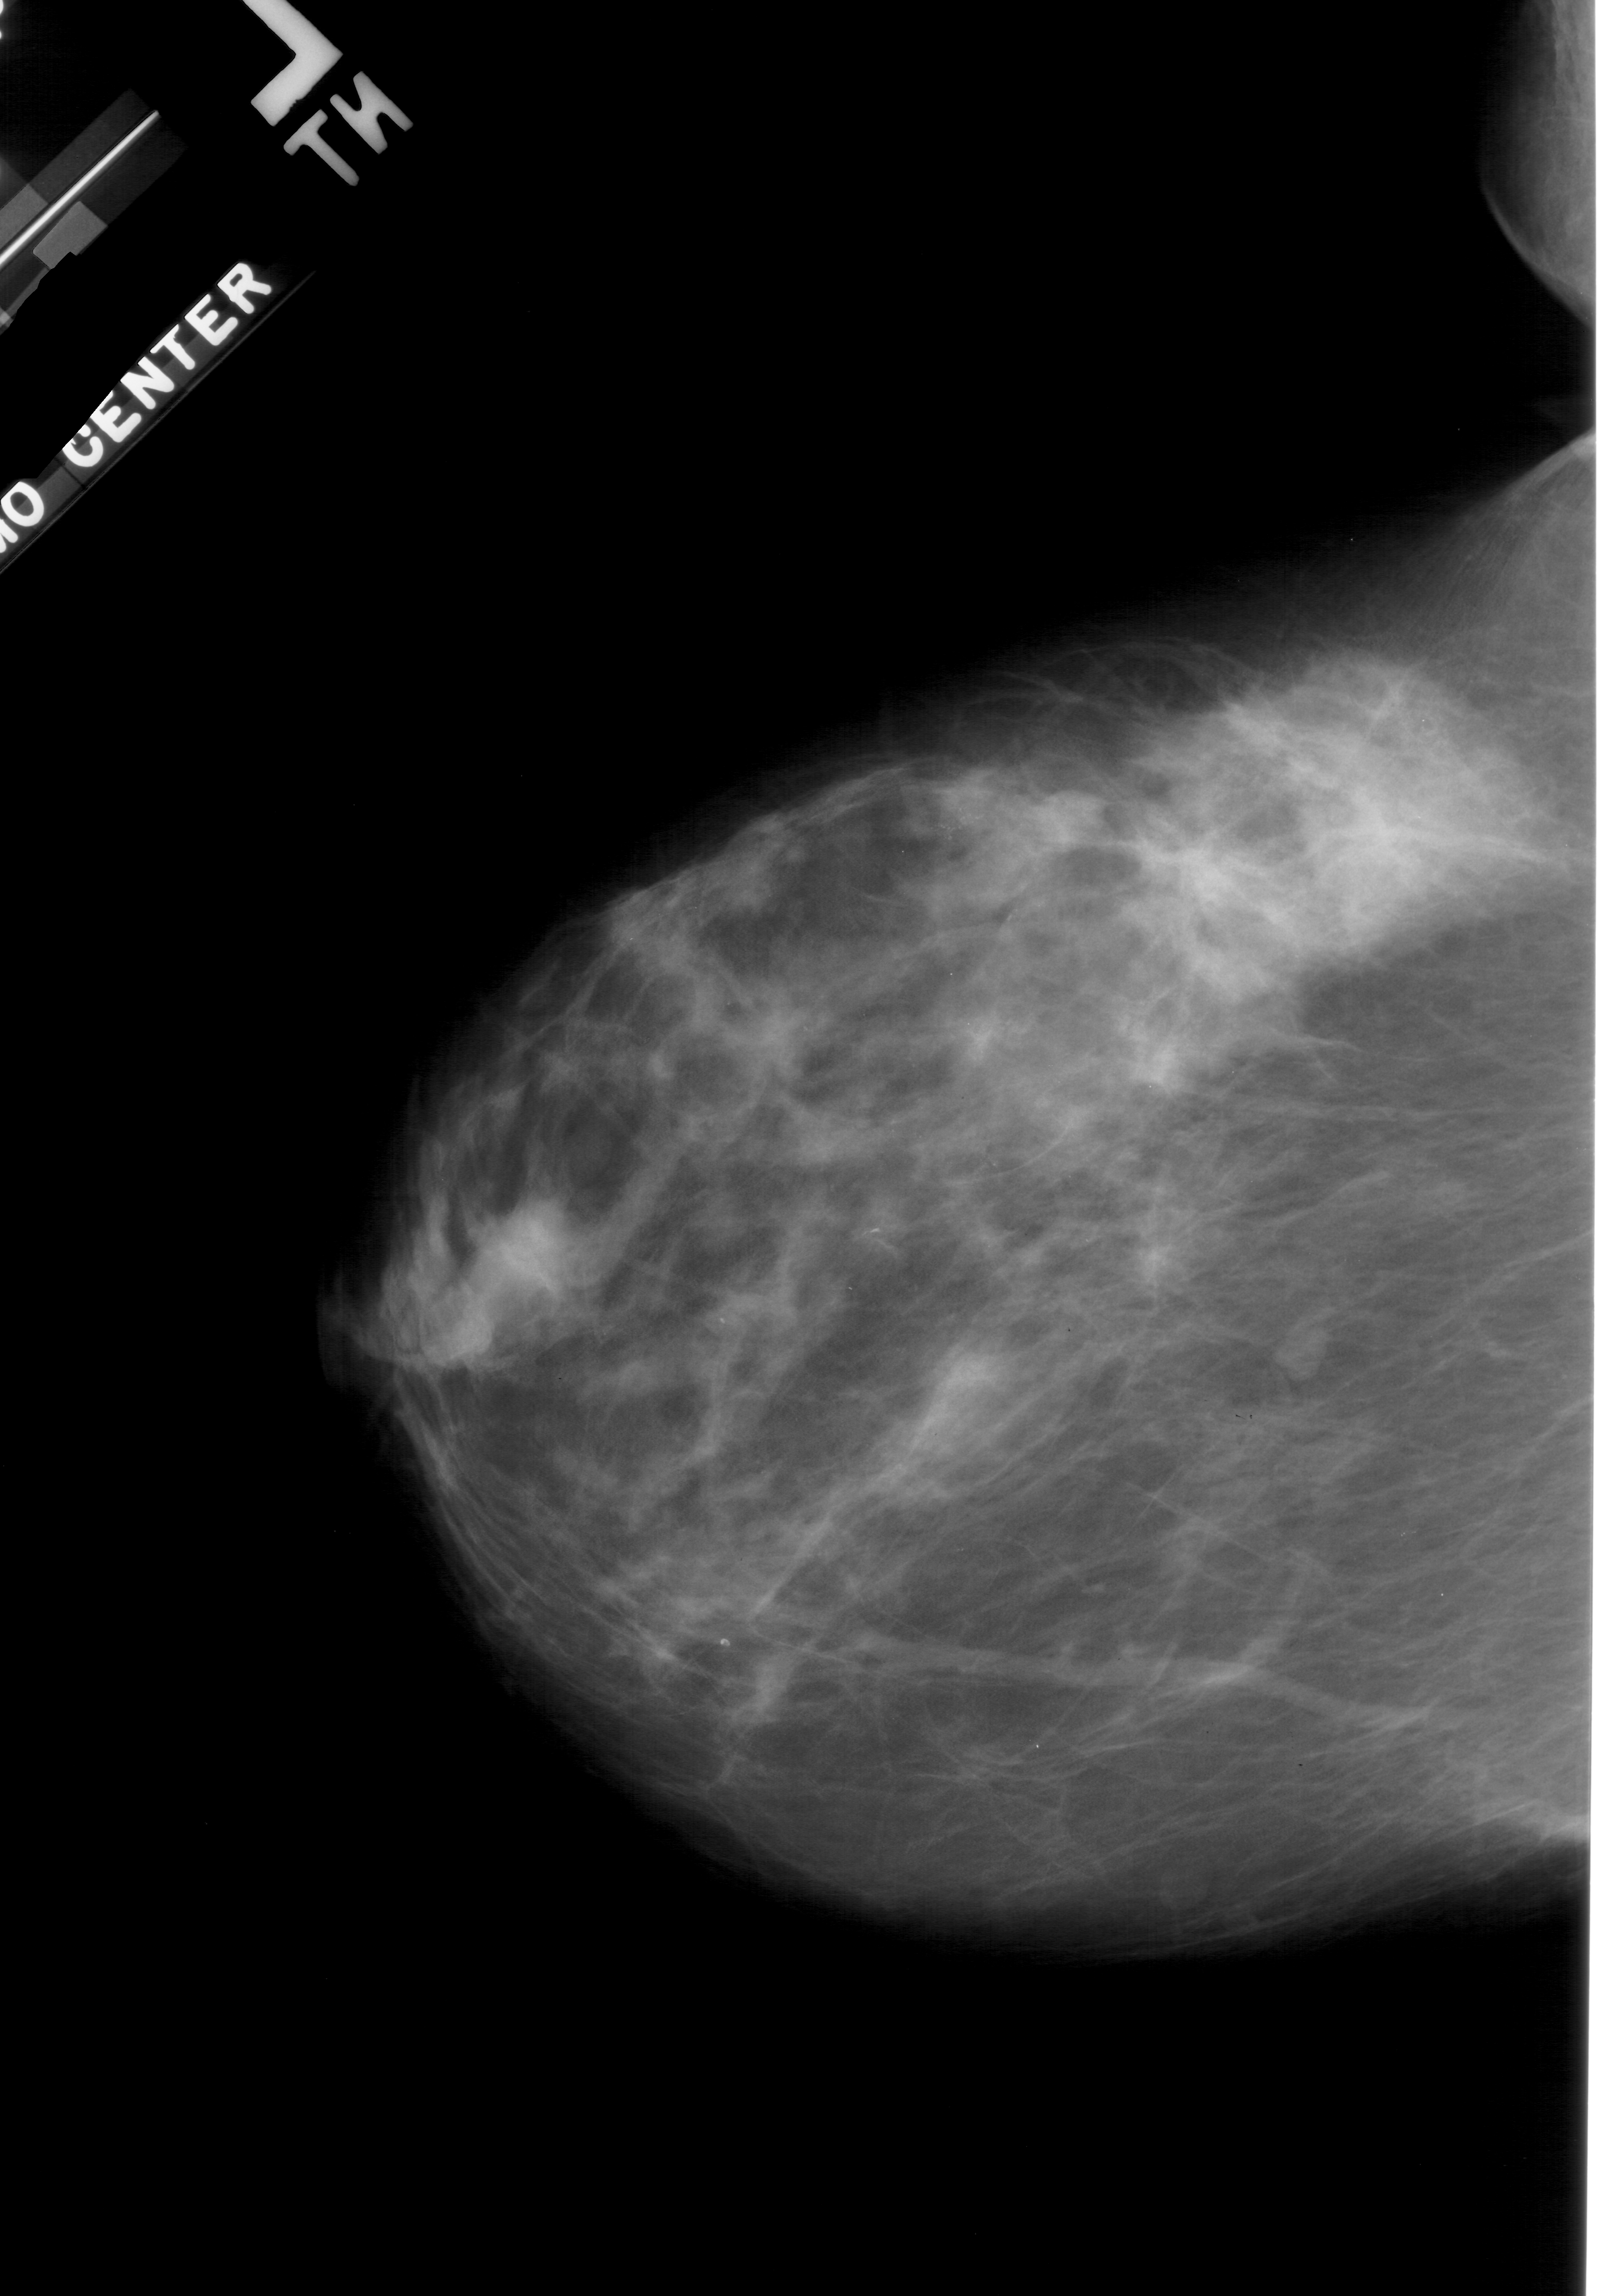
Mammogram (digitized film). Left breast. CC view. 1601 × 2296 image matrix.
Marked abnormalities (boxes around the expert regions of interest):
- calcifications, morphology pleomorphic, distribution clustered; BI-RADS assessment category 4; pathology result (as recorded, not read from the image): benign: bounding box (x1, y1, x2, y2) in pixels: (915, 776, 1039, 929)